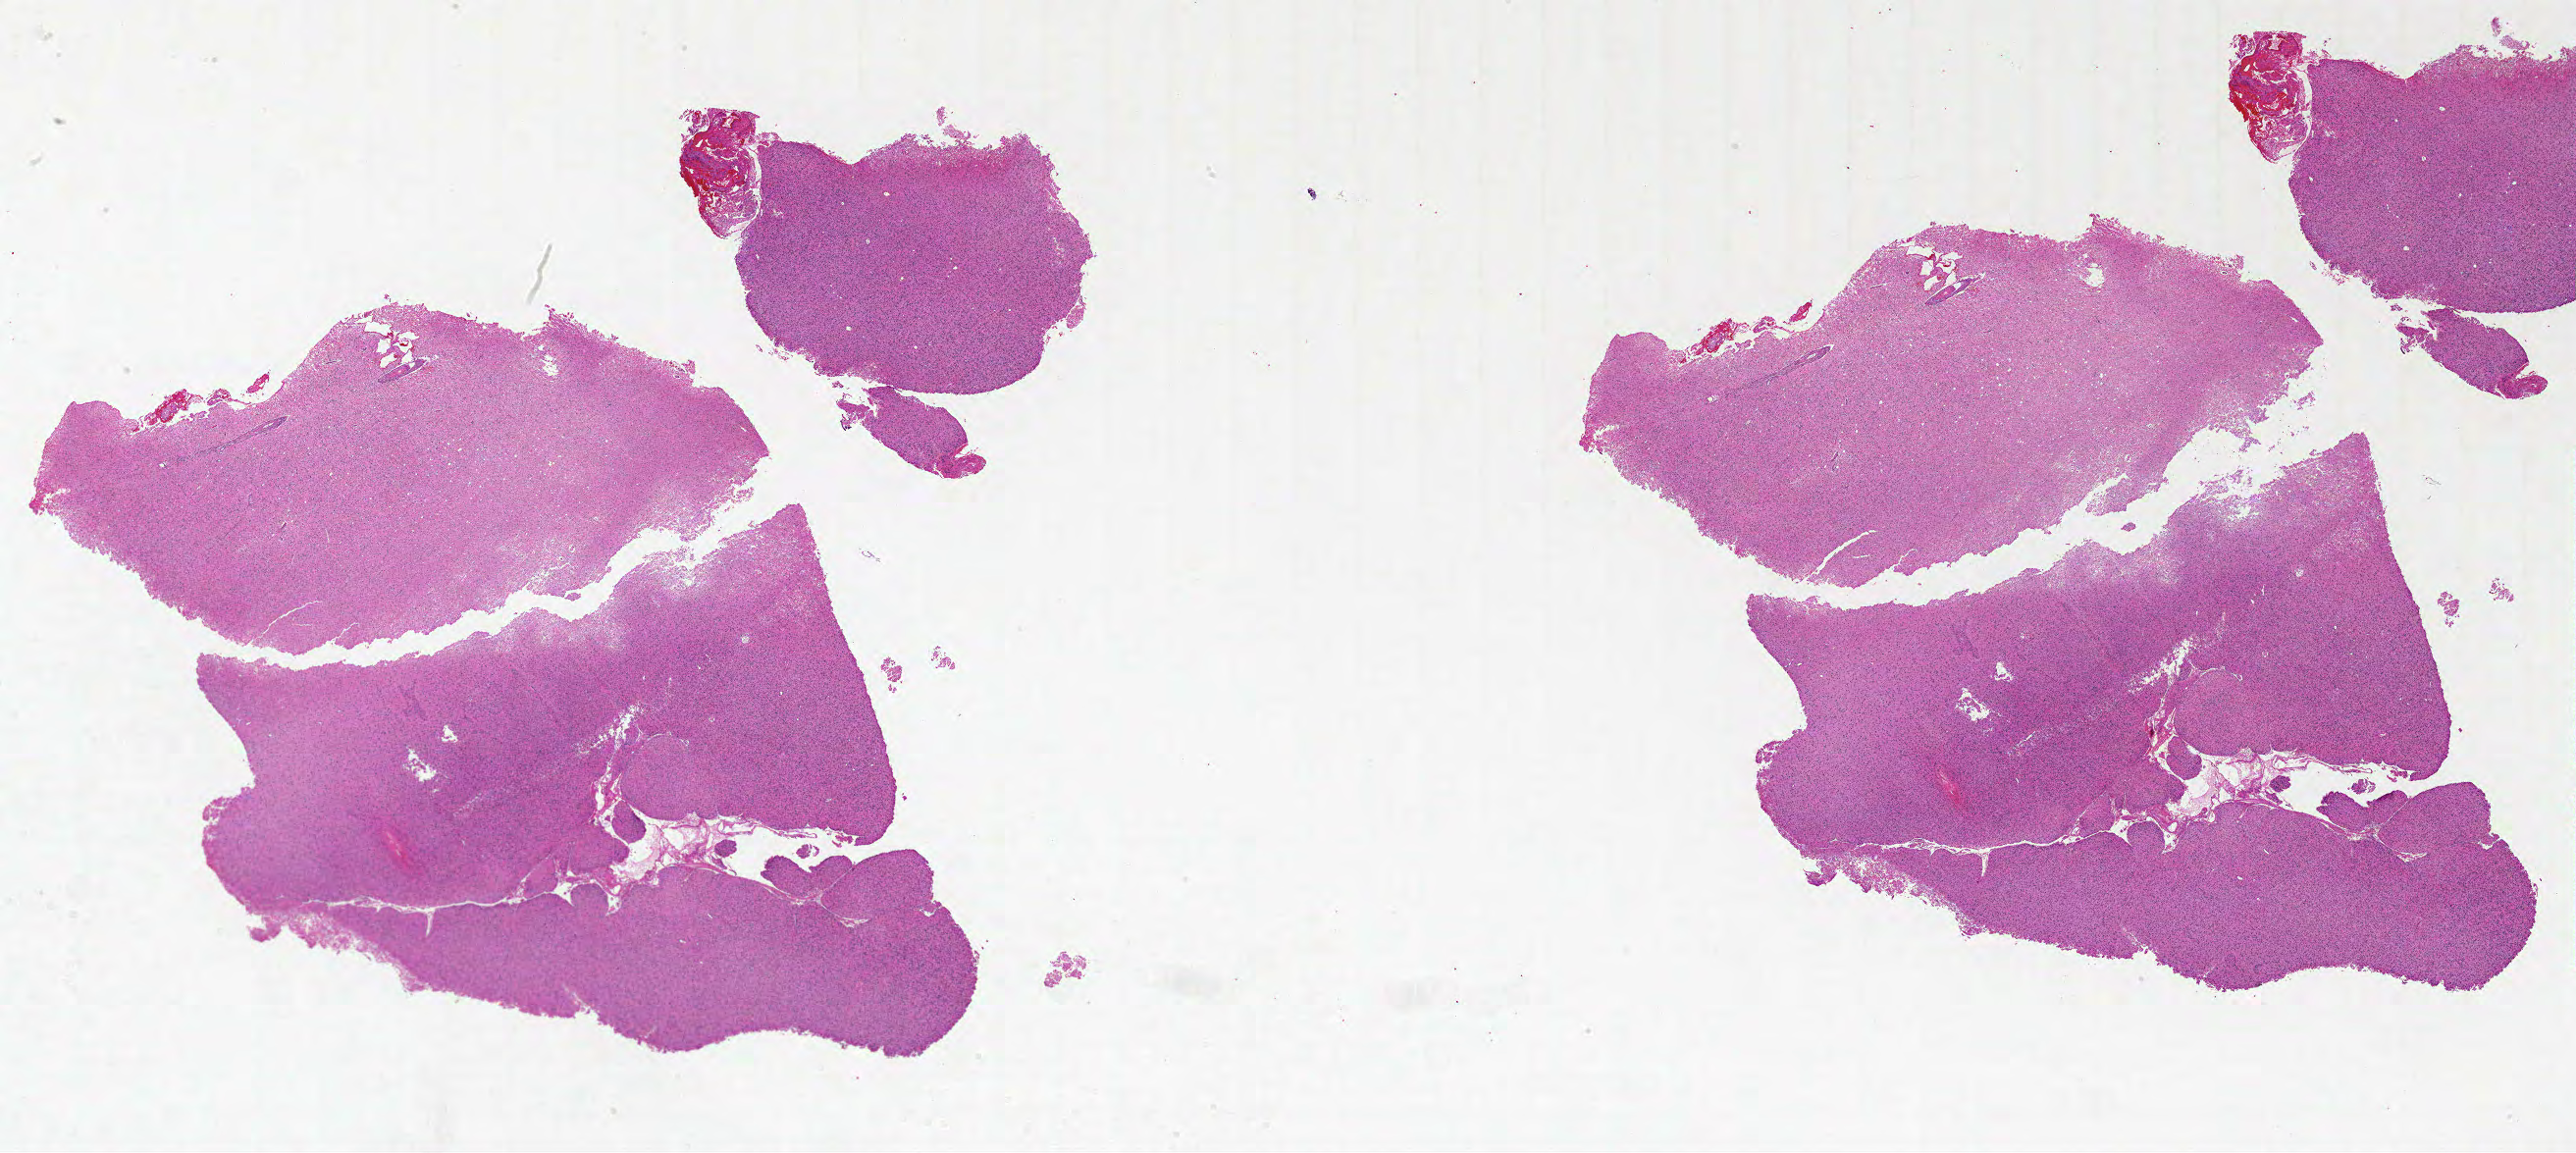
Whole-slide histology image, H&E, a low-resolution overview of the entire scanned area, about 42.0 x 18.8 mm; formalin-fixed paraffin-embedded (FFPE) diagnostic section; sample: primary tumour, brain. Male, age 76 years at initial diagnosis.
Pathologic diagnosis: Glioblastoma.